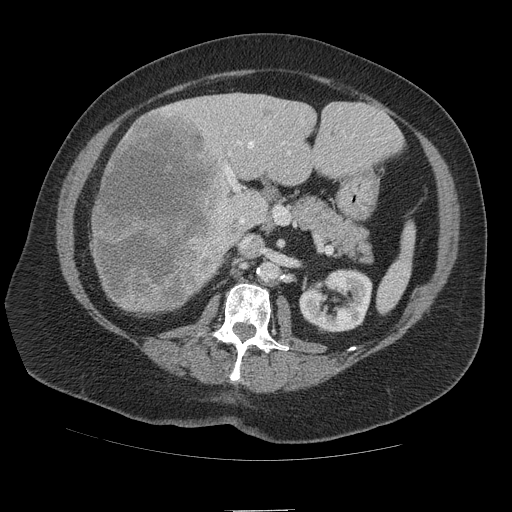
Contrast-enhanced abdominal CT (liver protocol), one axial slice; position 50 of 109 along the scan axis; reconstruction kernel STANDARD; soft-tissue window (W 400 / L 40 HU); 512 × 512 image matrix, field of view 420 × 420 mm. From the clinical record (not read from this slice): diagnosis: hepatocellular carcinoma (patient treated with transarterial chemoembolisation; whether this scan precedes or follows treatment is not stated here); TNM stage (as recorded): Stage-IVB; Child-Pugh class: A.
Structures marked on this image (semi-automatically segmented with operator editing):
- liver parenchyma outside the tumour (the mass and vessels are separate outlines, so this box may not span the whole liver): bounding box <92,92,402,312> (left, top, right, bottom; pixels)
- mass: <89,104,245,313>
- liver vessels: <224,141,291,191>